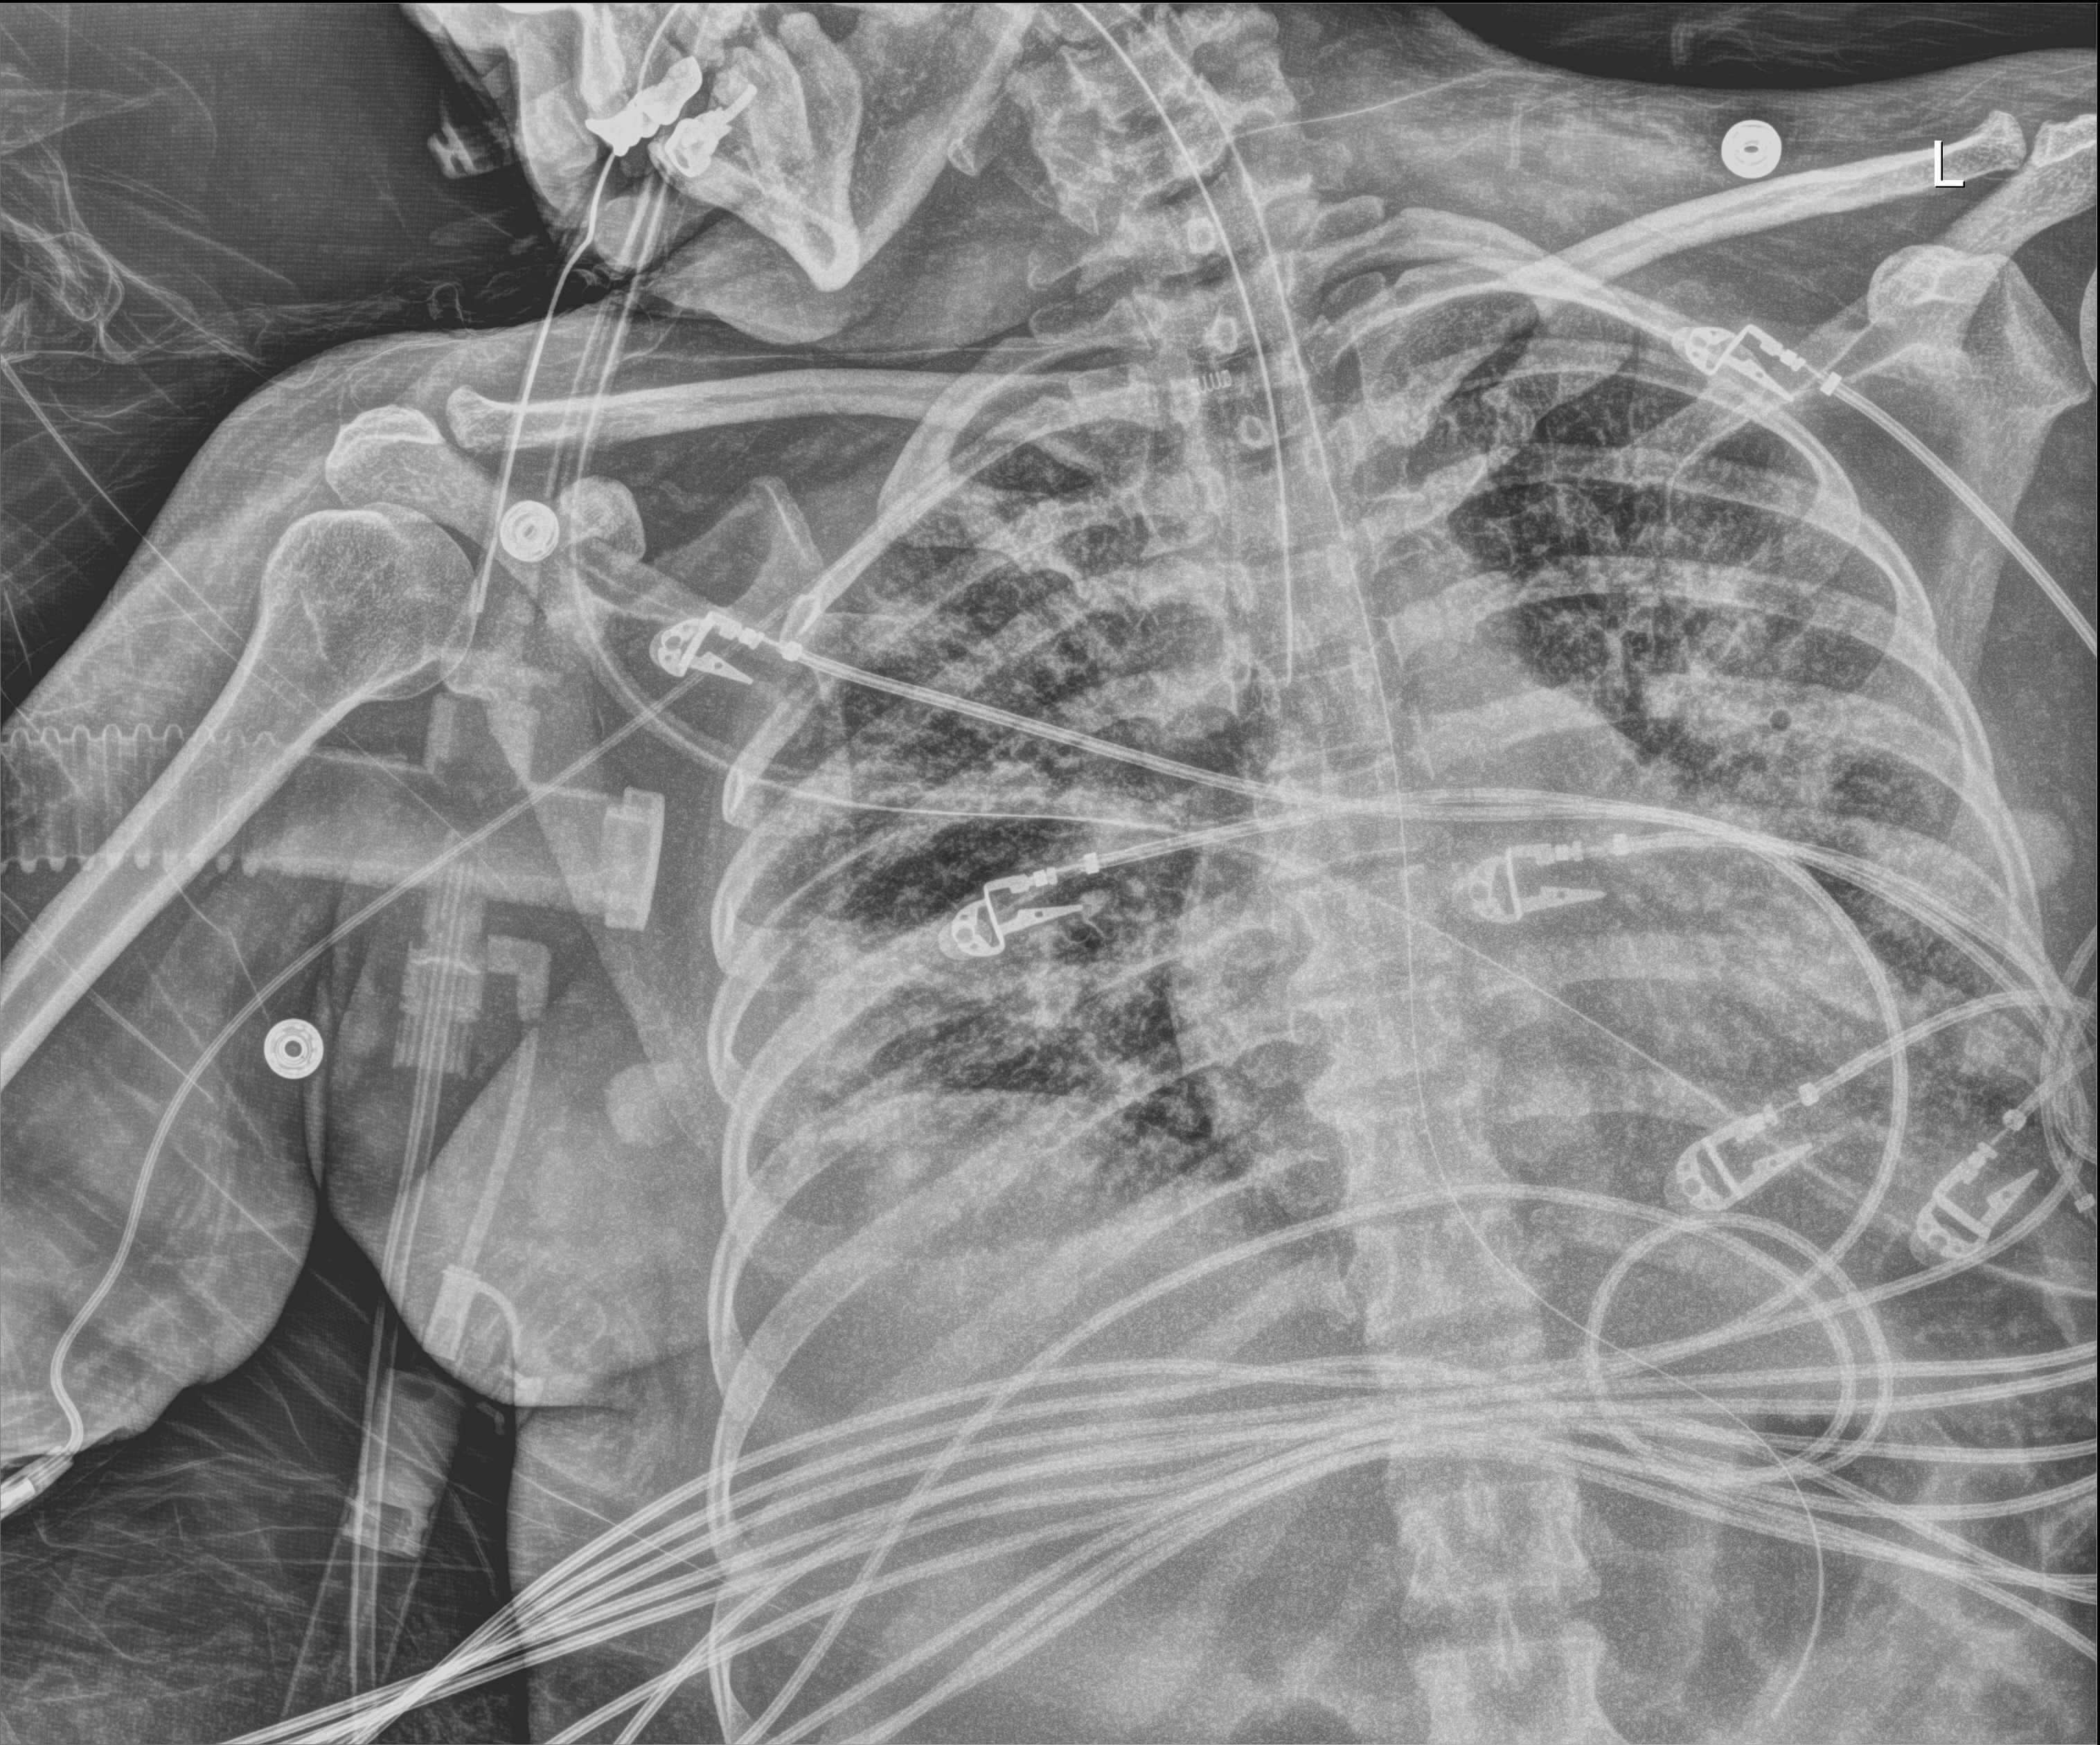
Portable chest radiograph. Female patient hospitalised with COVID-19, age 18–59 years.
From the hospital-stay record, not from the radiograph (when in the stay this image was taken is not recorded): admitted to intensive care during this hospital stay: yes.